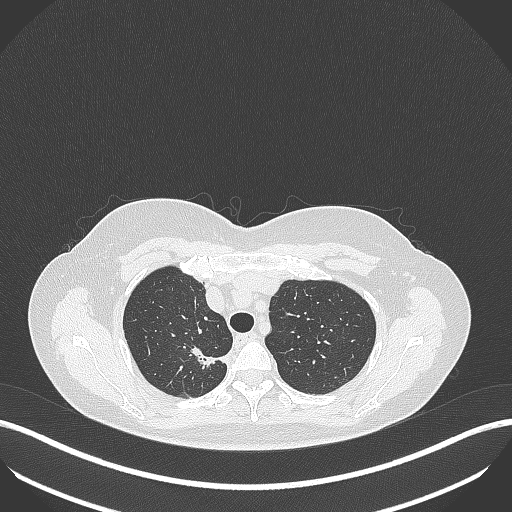
Chest CT, one axial slice; slice 315 of 386 in the series (ordered by position); reconstruction kernel B70f; lung window (W 1500 / L -600 HU); 512 × 512 image matrix, field of view 400 × 400 mm. Patient: female, 65 years. Case-level facts recorded for this patient, not image findings: clinical TNM (as recorded): T1b N0 M0.
Structures marked on this image (bounding box drawn by a radiologist):
- lung tumour (recorded histology: adenocarcinoma): bounding box [x1, y1, x2, y2] px = [189, 341, 231, 369]